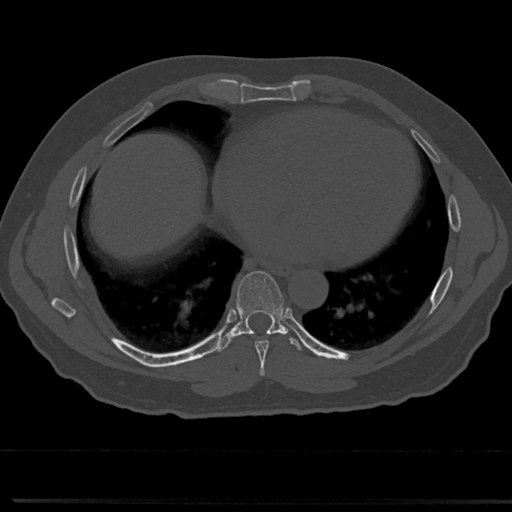
CT including the spine, one axial slice. Position 373 of 817 along the scan axis. Reconstruction kernel Br40s/3. 120 kVp. Bone window (W 1800 / L 400 HU). 512 × 512 image matrix, field of view 355 × 355 mm. Patient: male, 61 years. Case-level facts recorded for this patient, not image findings: primary cancer: prostate.
Outlined on this slice (semi-automatic segmentation, software-assisted and operator-edited):
- T7 vertebra: bounding box (x1, y1, x2, y2) in pixels: (235, 271, 288, 357)
- T8 vertebra: (237, 325, 282, 333)